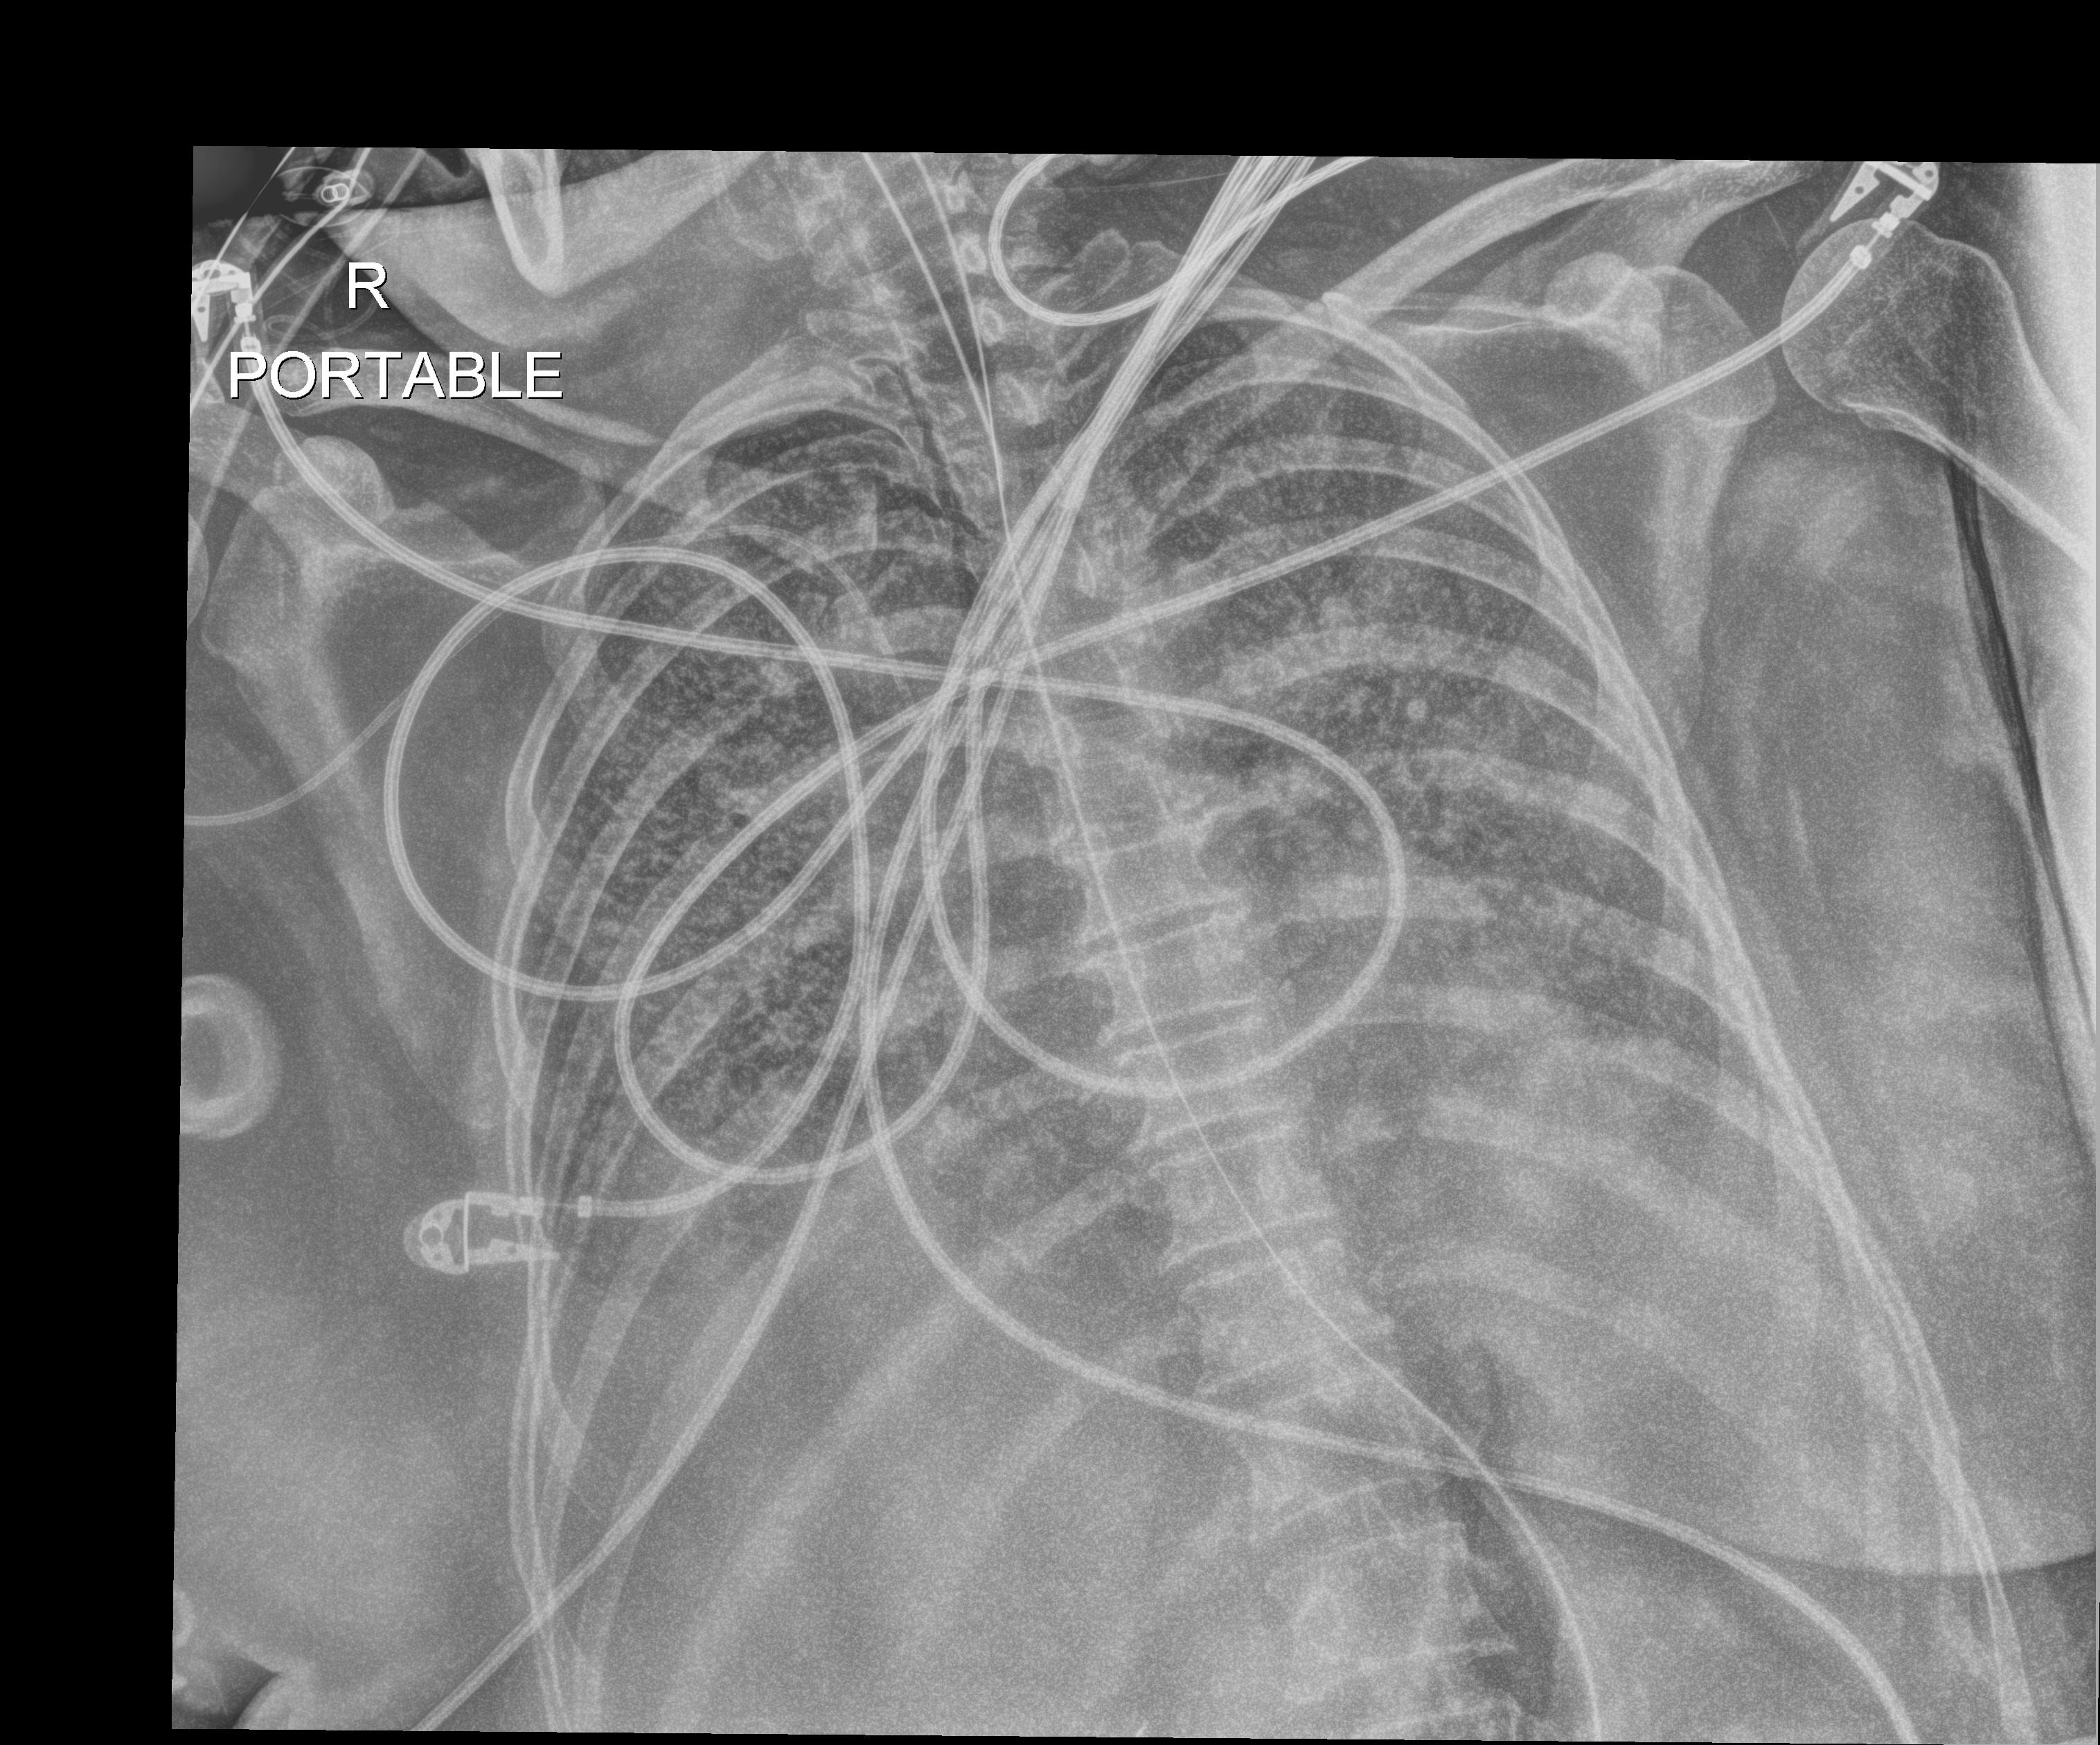
Portable chest radiograph; anteroposterior (AP) projection. Patient hospitalised with COVID-19; female, aged 18–59 years.
Hospital-stay facts (about this admission, not read from this image; timing relative to this image not recorded):
- length of hospital stay: 95 days
- mechanically ventilated during this hospital stay: yes
- admitted to intensive care during this hospital stay: yes